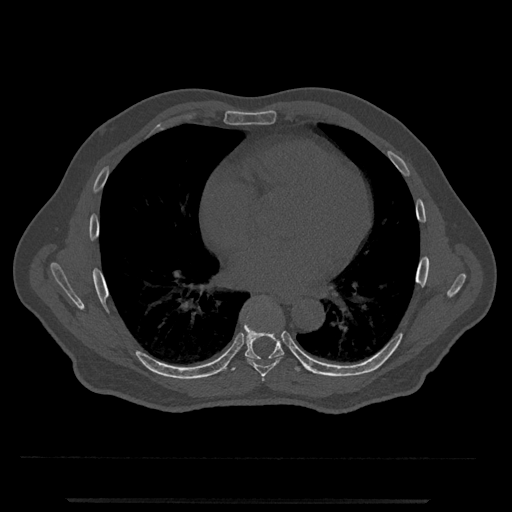
CT including the spine, one axial slice. Slice 656 of 797 in the series (ordered by position). Reconstruction kernel Br40s/3. 120 kVp. Bone window (W 1800 / L 400 HU). 0.5 mm slice thickness. 512 × 512 image matrix, field of view 419 × 419 mm. Patient: male, 63 years. Case-level facts recorded for this patient, not image findings: primary cancer: prostate.
Outlined on this slice (semi-automatic segmentation, software-assisted and operator-edited):
- T7 vertebra: bounding box <247,356,282,381> (left, top, right, bottom; pixels)
- T8 vertebra: <229,304,301,373>